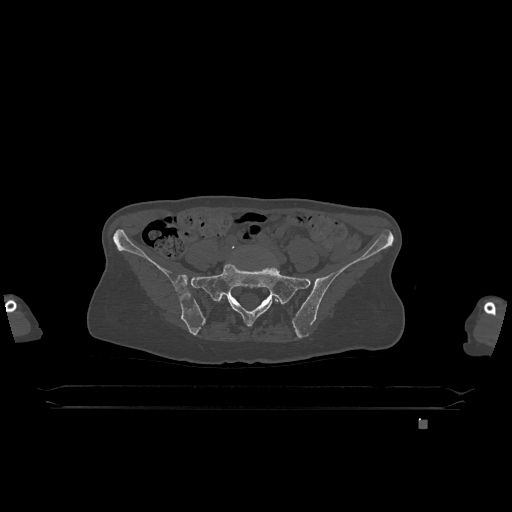
CT including the spine, one axial slice; slice 198 of 1317 in the series (ordered by position); bone window (W 1800 / L 400 HU); 0.5 mm slice thickness; 512 × 512 image matrix, field of view 500 × 500 mm. Female patient, age 74 years. From the clinical record (not read from this slice): primary cancer: lung.
Structures marked on this image (semi-automatically segmented with operator editing):
- L5 vertebra: bounding box [x1, y1, x2, y2] px = [221, 296, 278, 303]